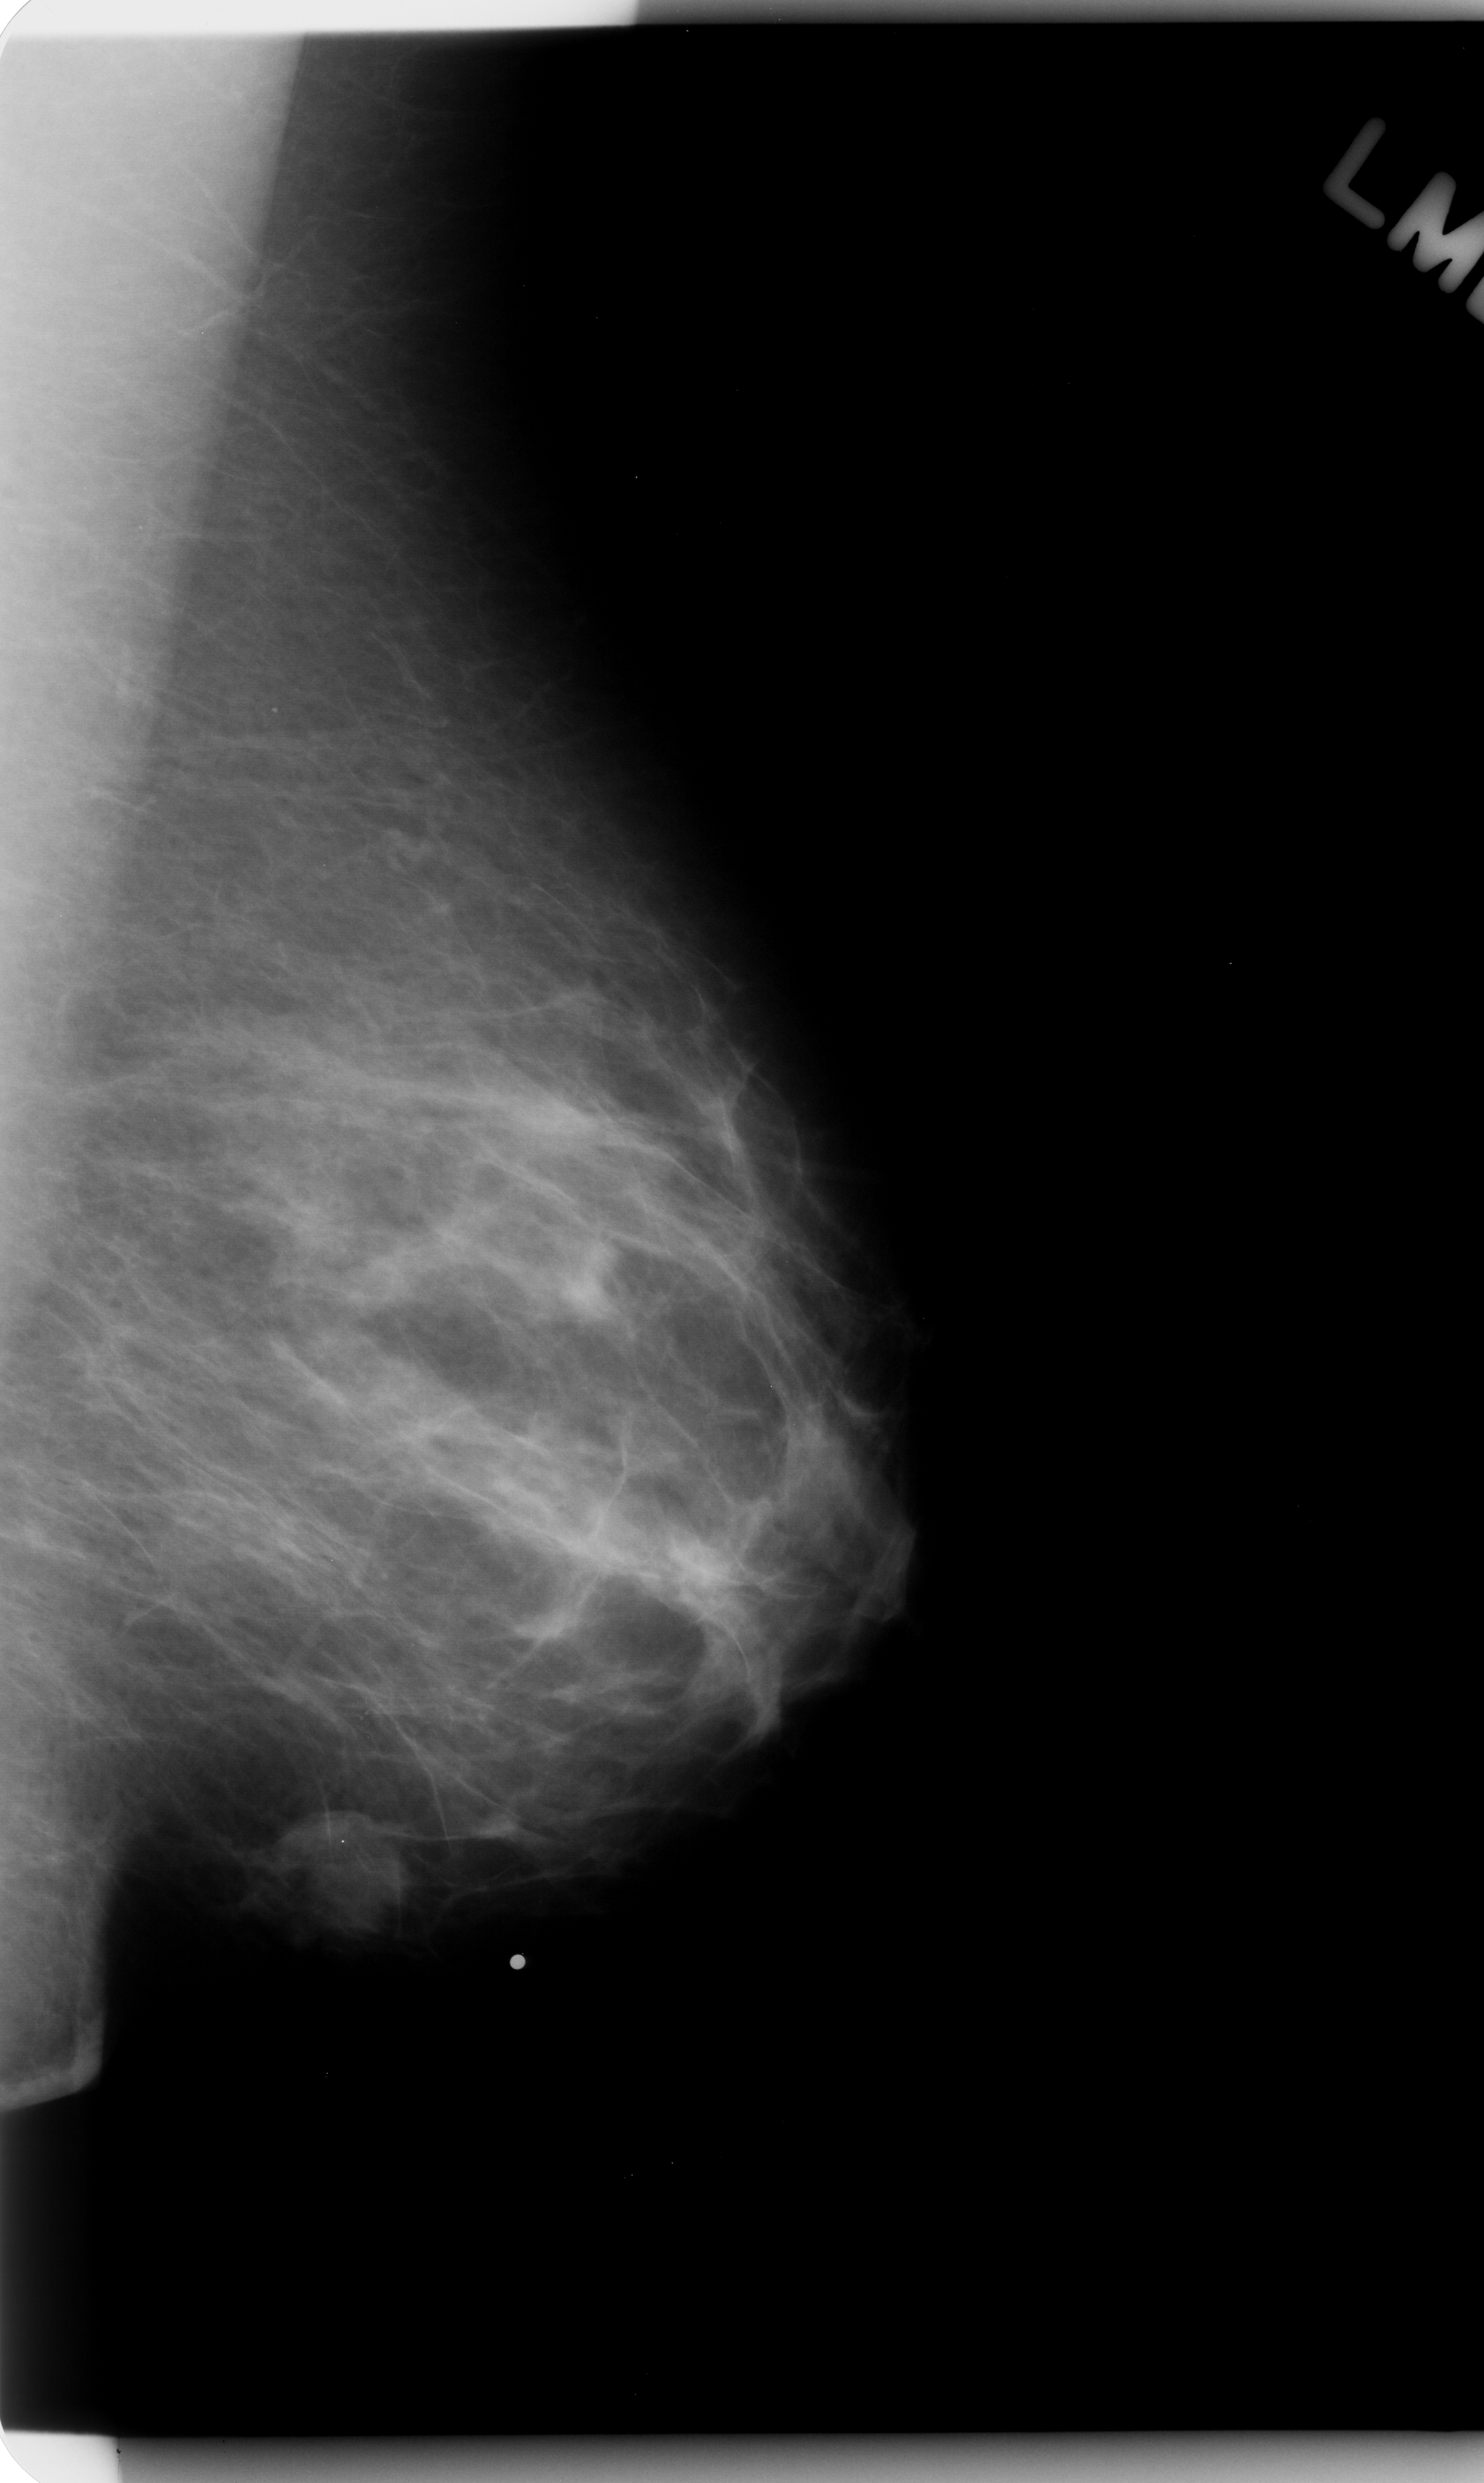
Digitized screen-film mammogram, left breast, mediolateral oblique (MLO) view, BI-RADS breast density category 2 (scale 1–4).
- Finding: mass, shape lobulated, margins microlobulated; BI-RADS assessment category 5; pathology result (as recorded, not read from the image): malignant.